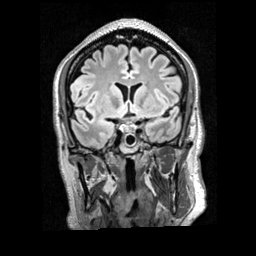
Brain MRI from a brain-tumour surgery series, one coronal slice; slice 121 of 200 in the series (ordered by position); T2 FLAIR; 256 × 256 image matrix, field of view 256 × 256 mm. Case-level facts recorded for this patient, not image findings: histopathology: Glioblastoma; WHO grade: 4; IDH mutation: no; tumour location: Right Frontal.
Outlined on this slice (manually delineated by an expert):
- tumour: box from (x=70, y=74) to (x=93, y=88) px